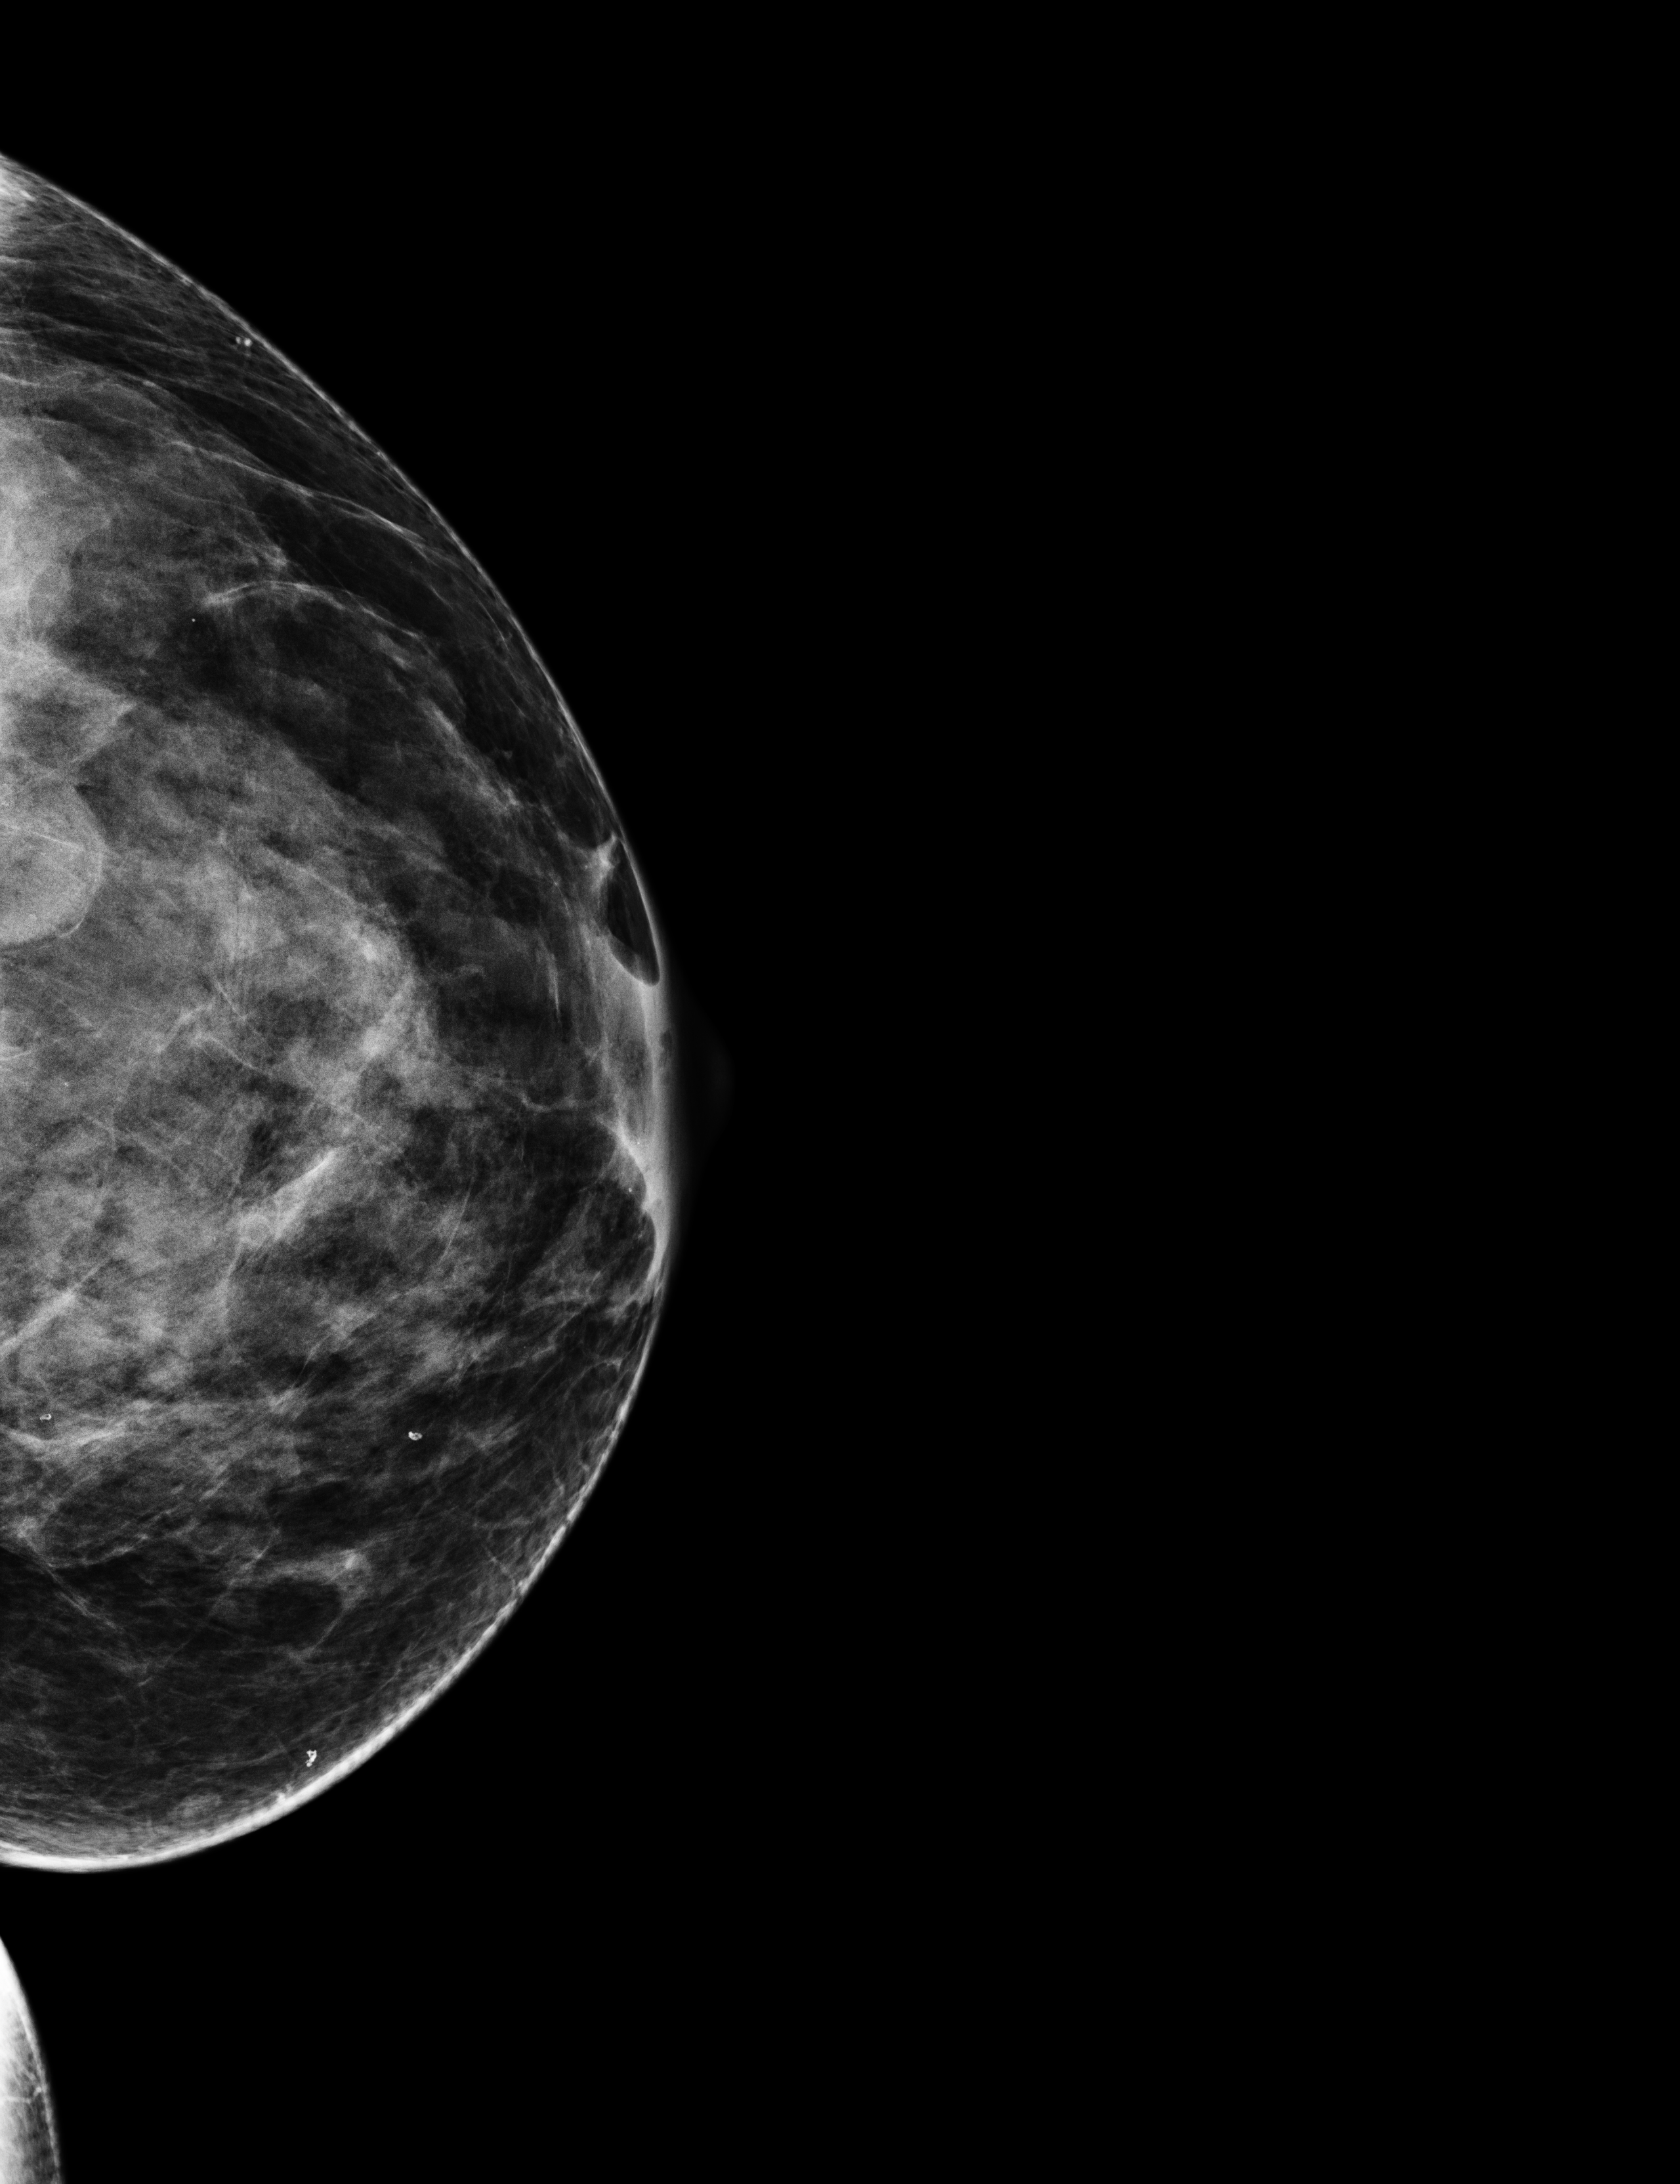
Screening examination; compressed breast thickness 54 mm.
Image type: full-field digital mammogram. Breast: left. Projection: CC view.